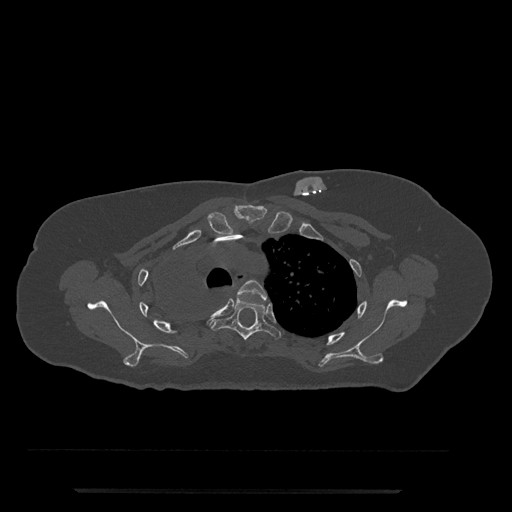
CT including the spine, one axial slice. Position 599 of 797 along the scan axis. 120 kVp. Bone window (W 1800 / L 400 HU). 0.5 mm slice thickness. 512 × 512 image matrix, field of view 440 × 440 mm. Patient: female, 51 years. Case-level facts recorded for this patient, not image findings: primary cancer: neuro.
Structures marked on this image (semi-automatically segmented with operator editing):
- T3 vertebra: bounding box [x1, y1, x2, y2] px = [238, 280, 267, 302]
- T4 vertebra: [210, 299, 281, 341]